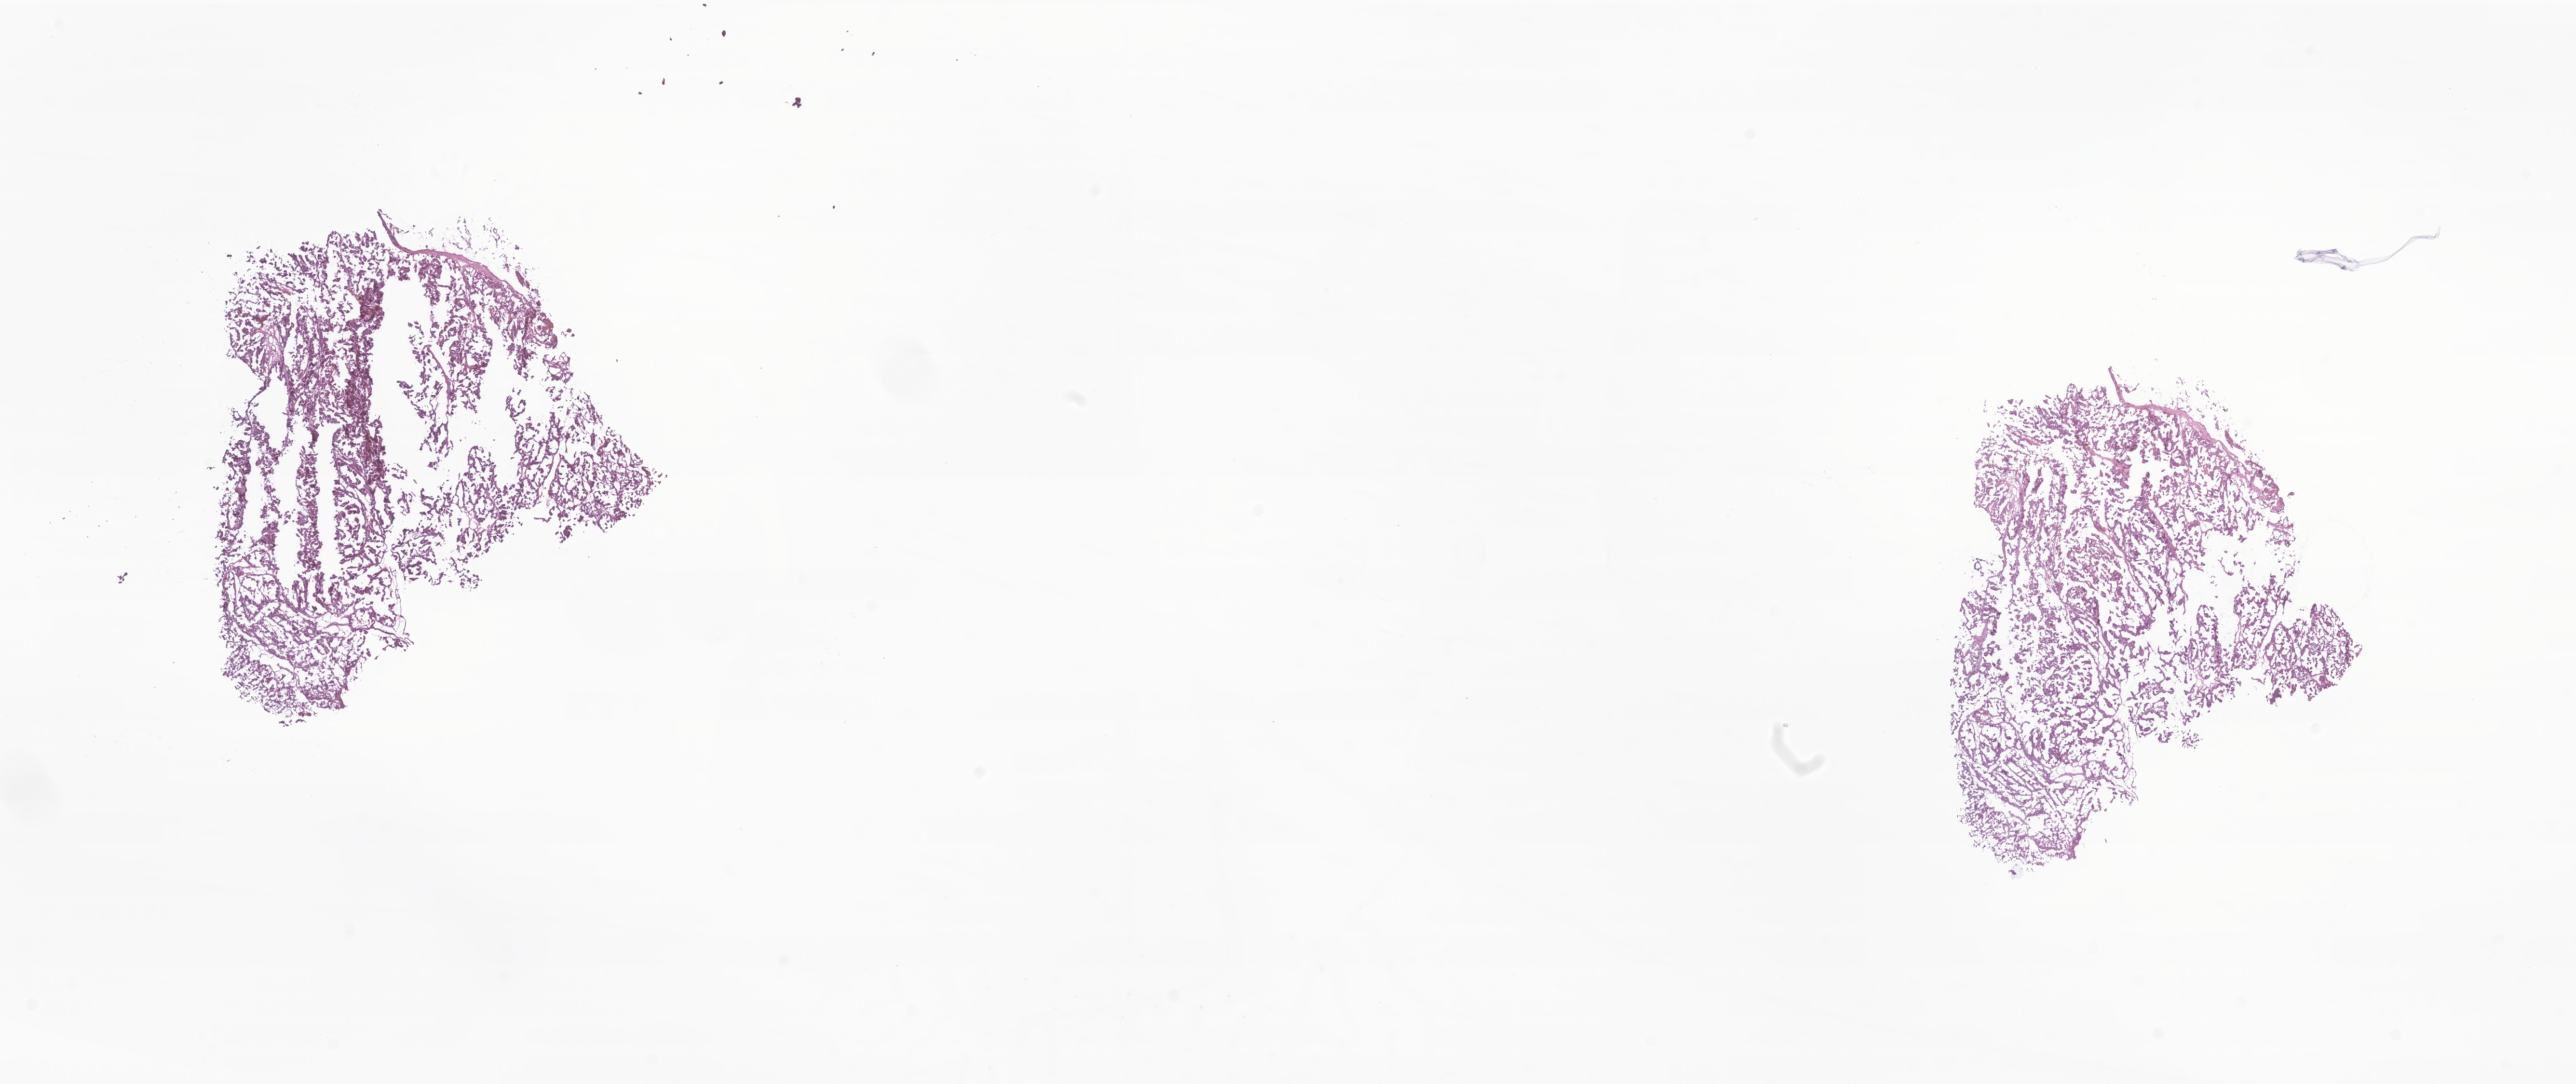
Hematoxylin and eosin (H&E) whole-slide image of tumor tissue from the cerebral ventricle — a low-resolution overview of the entire scanned area, about 22.5 x 9.5 mm; frozen section. Patient female; age 138 days.
Recorded diagnosis: Choroid plexus papilloma, NOS.